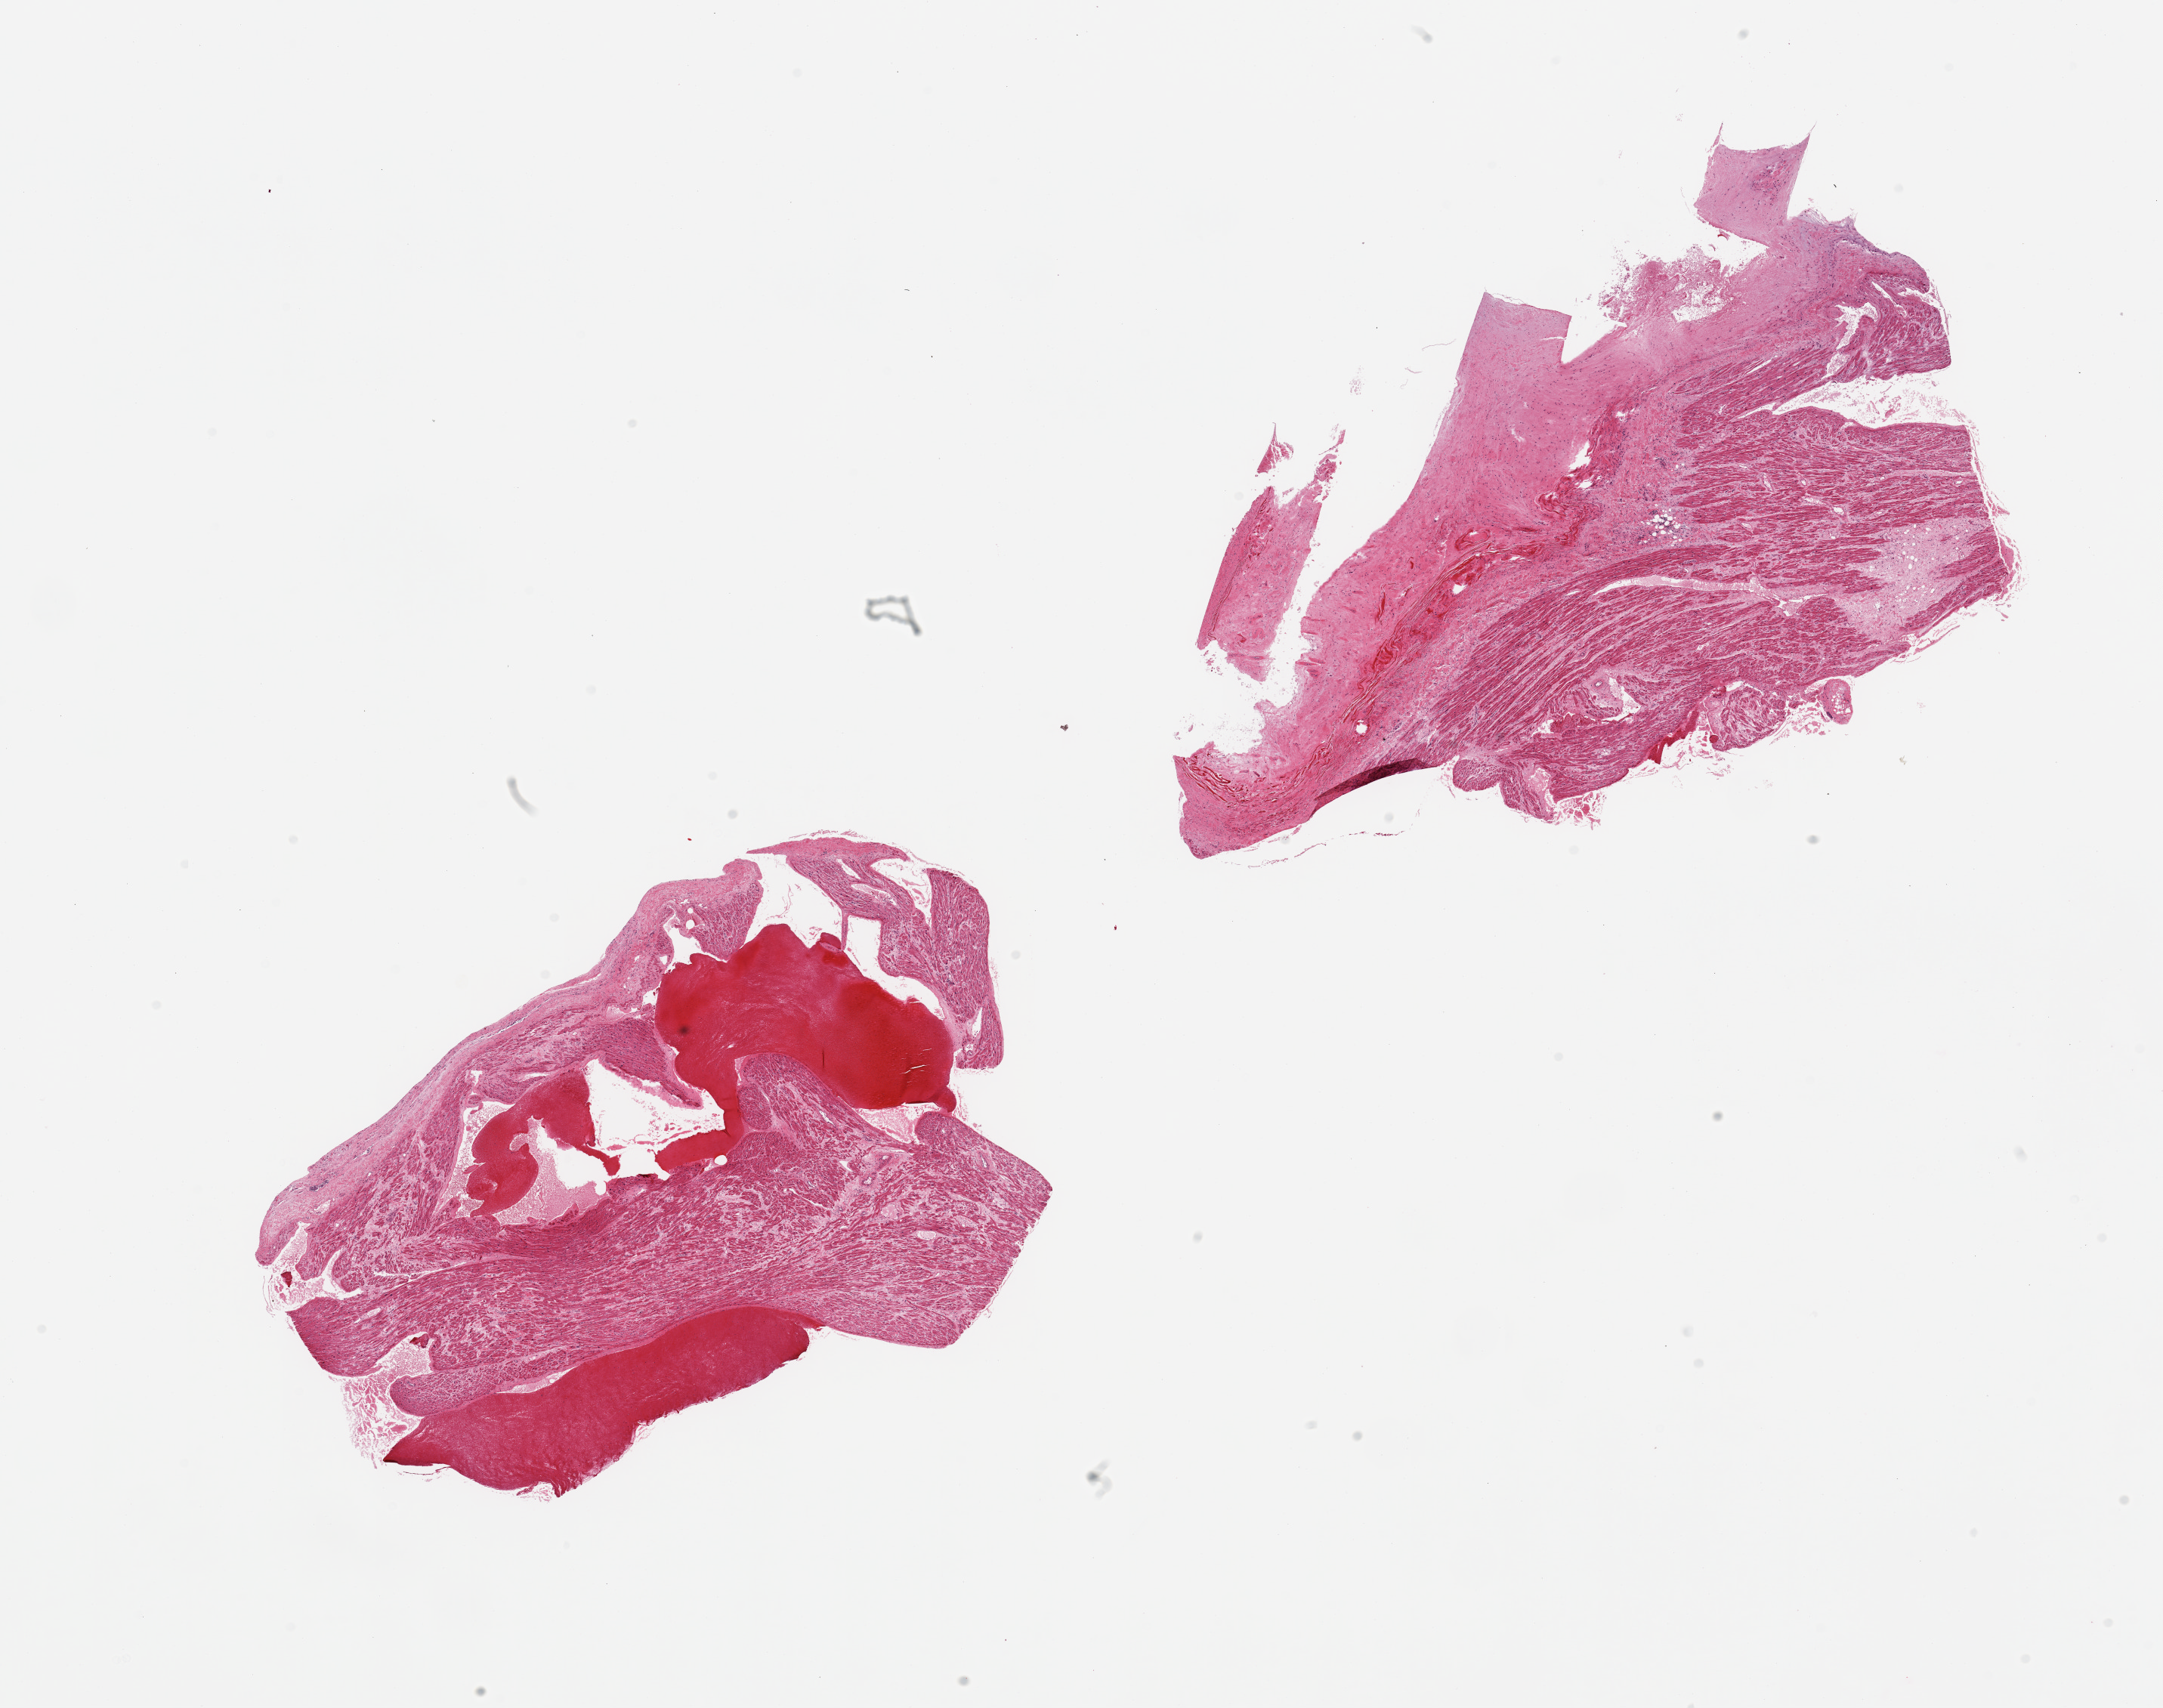
Digitized haematoxylin and eosin-stained section, brightfield — a low-resolution overview of the entire scanned area, about 22.6 x 17.9 mm (acquisition: 20x scan). PAXgene-fixed paraffin-embedded (PFPE) section. Section of auricular appendage (target tissue). Donor tissue sample. Female donor.
• review note (as recorded): 2 pieces, vascular congestion